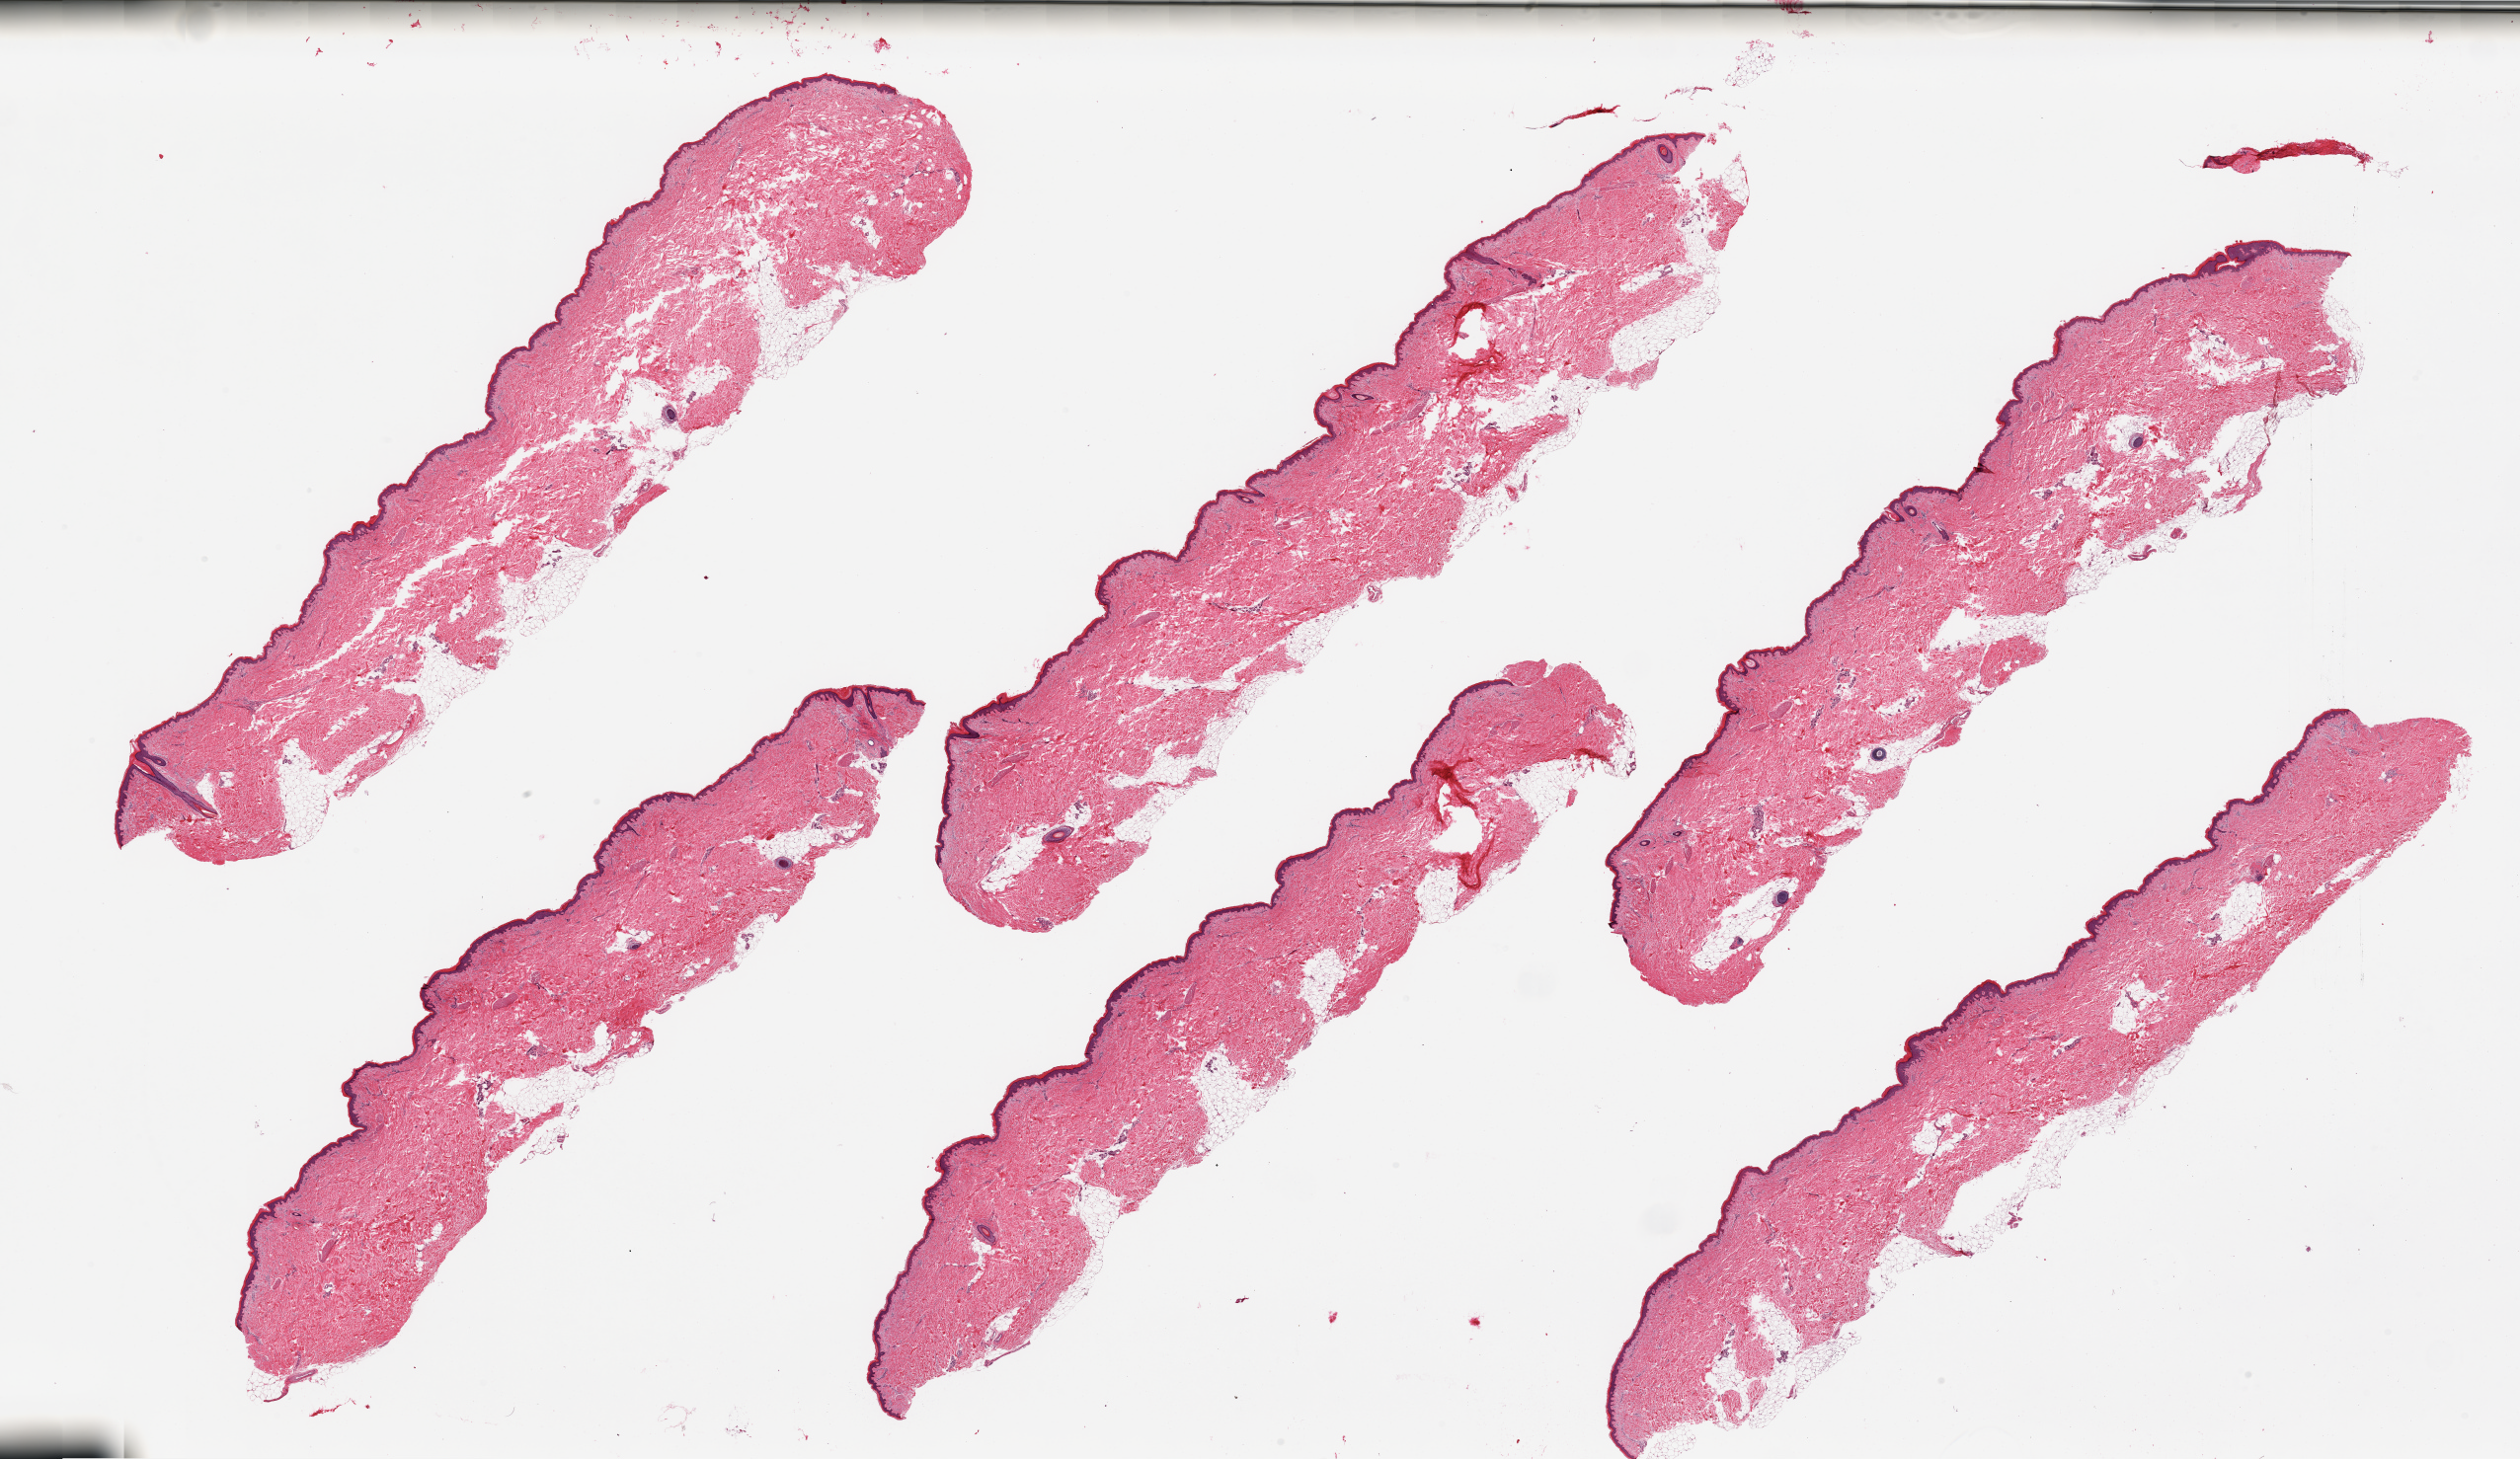
Whole-slide image, hematoxylin and eosin (H&E) stain, brightfield, a low-resolution overview of the entire scanned area, about 40.4 x 23.4 mm; PAXgene-fixed, paraffin-embedded tissue; target tissue: skin of lower leg; donor tissue sample. Donor: female.
Review note (as recorded): 6 pieces. well dissected.